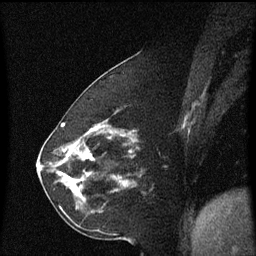
Breast MRI (dynamic contrast-enhanced), one sagittal slice; position 22 of 60 along the scan axis; dynamic contrast-enhanced series, image 2 of 3 at this slice position (ordered by acquisition); 1.5 T; TE 4.2 ms, TR 8.4 ms; 2.2 mm slice thickness; 256 × 256 image matrix, field of view 200 × 200 mm. Female patient, age 60 years. From the clinical record (not read from this slice): setting: breast cancer imaged before/during neoadjuvant chemotherapy; receptor status: triple-negative.
Annotated regions visible in this slice (semi-automatically segmented with operator editing):
- analysis volume of interest (the breast-tissue region the enhancement analysis was run in; not a lesion): bounding box [x1, y1, x2, y2] px = [68, 142, 131, 213]
- tumour enhancement mask (voxels above the 70 % enhancement threshold inside the analysis volume of interest): [68, 154, 126, 185]